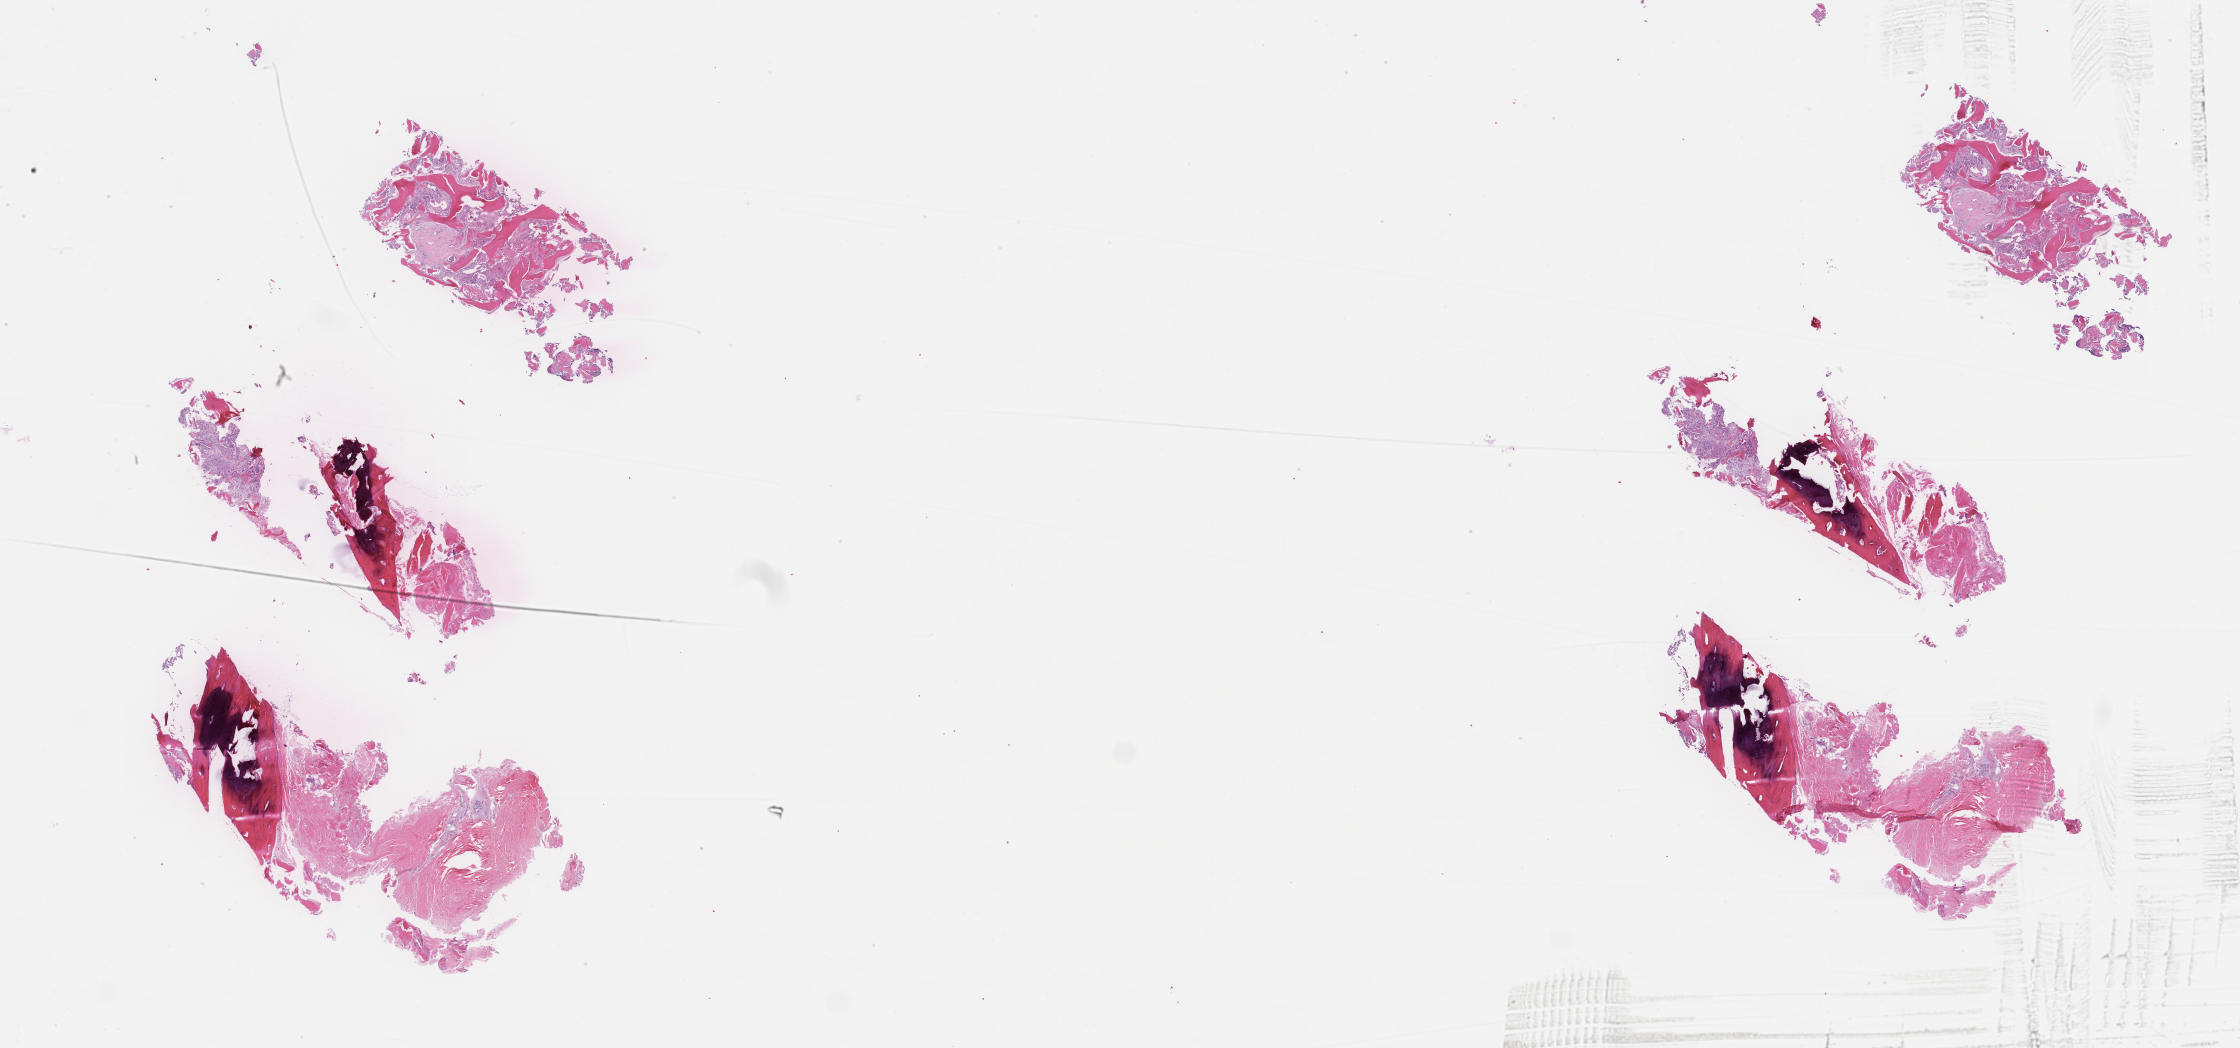
Hematoxylin and eosin (H&E) whole-slide image — a low-resolution overview of the entire scanned area, about 36.2 x 16.9 mm; formalin-fixed paraffin-embedded section; site: breast; specimen time point: archival tissue. Patient sex: female.
This section: primary tumor. Diagnosis: Invasive Breast Carcinoma.